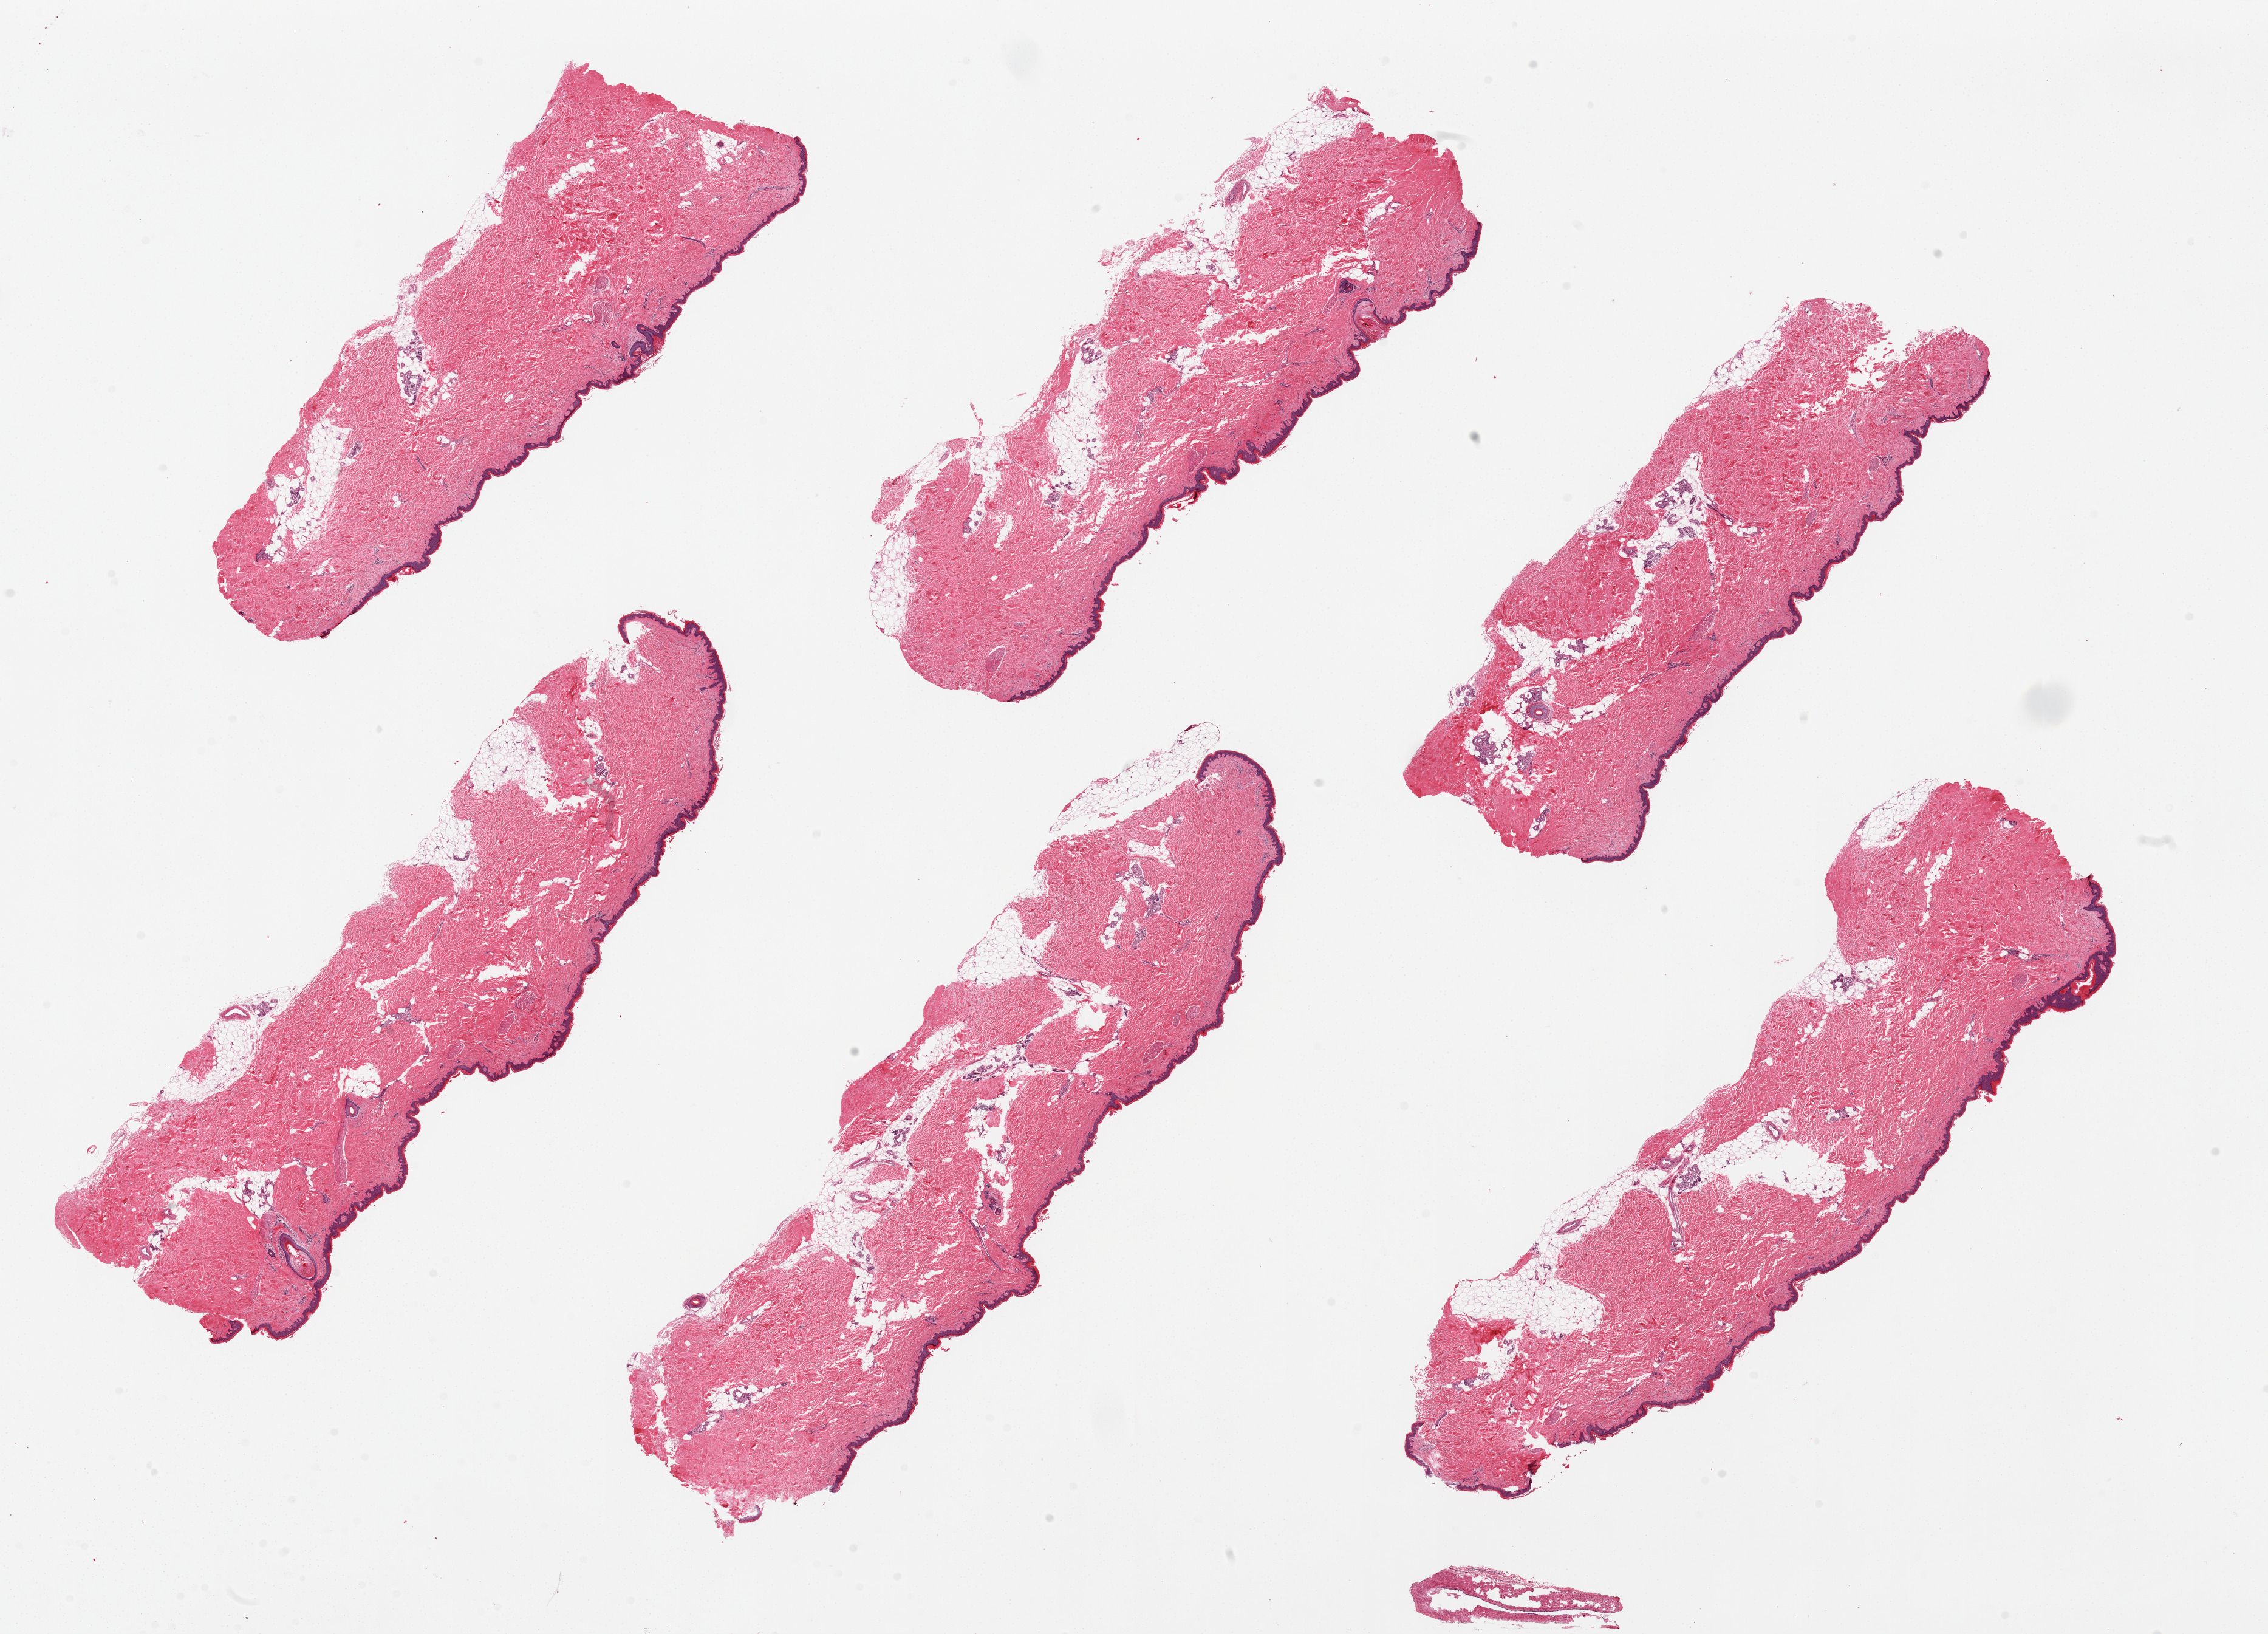
Haematoxylin and eosin whole-slide image, a low-resolution overview of the entire scanned area, about 29.5 x 21.3 mm (acquisition: 20x scan), PAXgene-fixed paraffin-embedded (PFPE) section, sampled site (target tissue): skin of lower leg, donor tissue sample. Donor sex: male.
Review note (as recorded): 1 piece; well trimmed, comparable to 25 block.